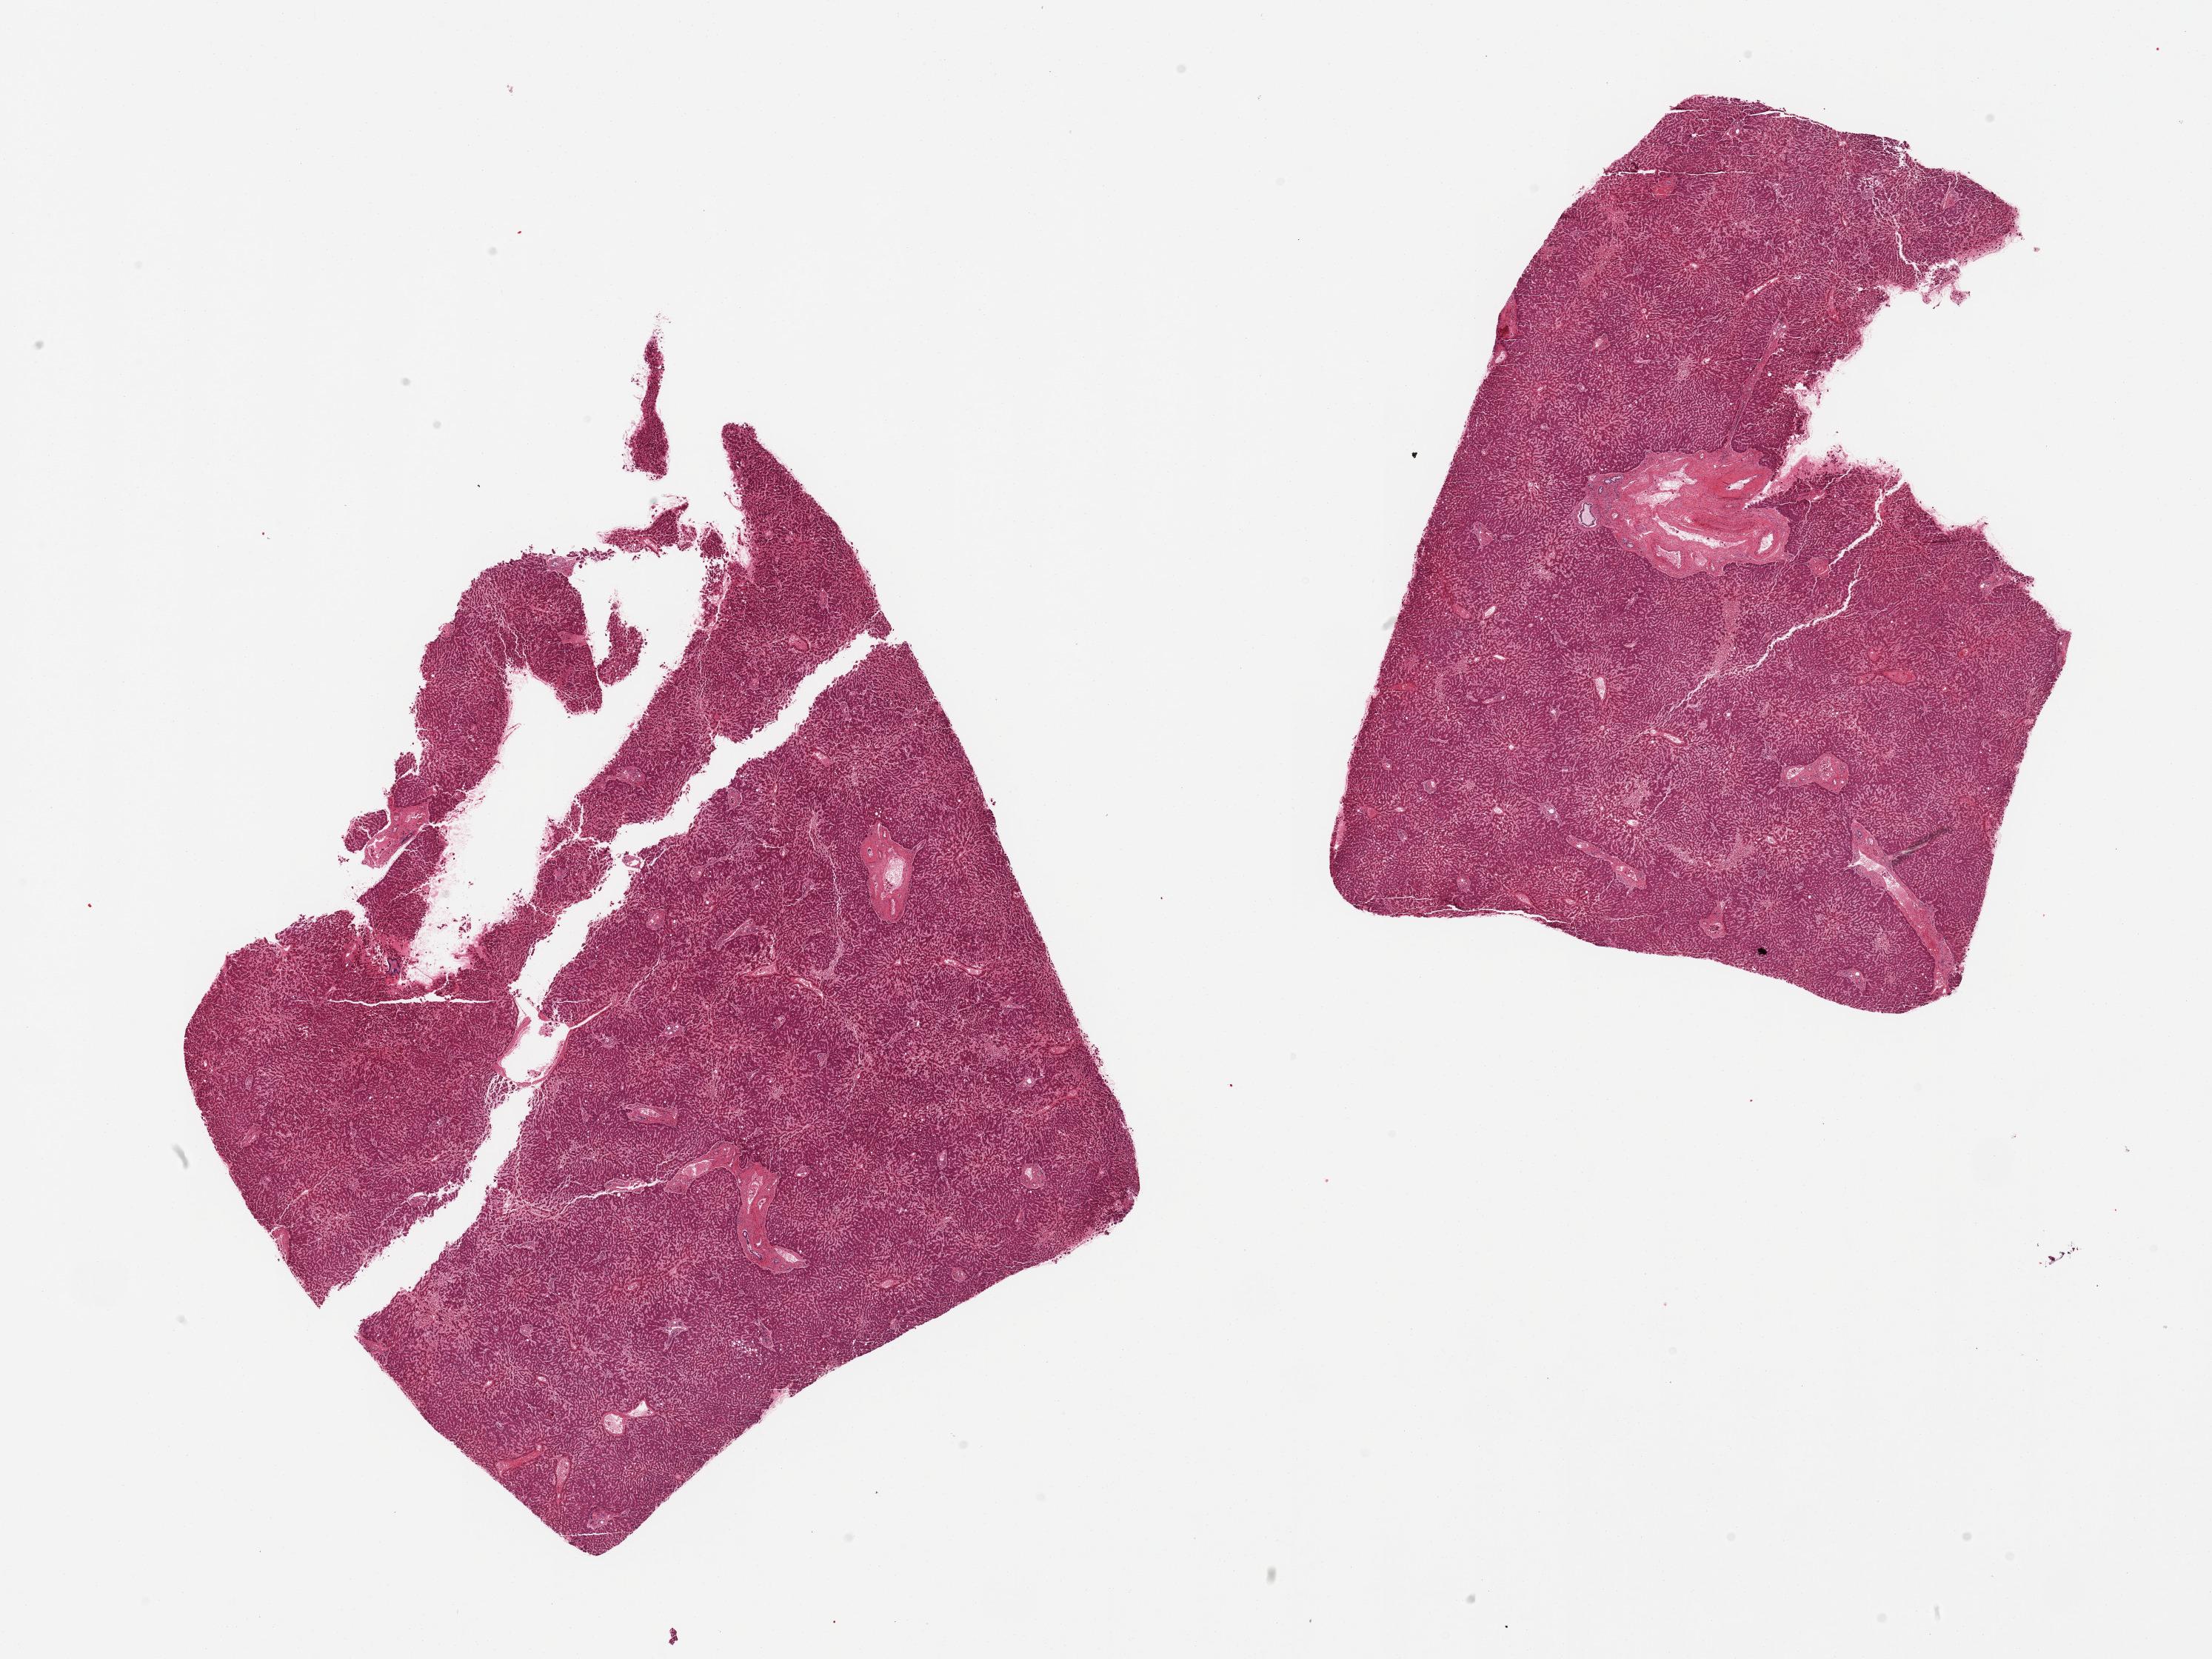
Digitized hematoxylin and eosin (H&E)-stained section — a low-resolution overview of the entire scanned area, about 23.6 x 17.7 mm (from a 20x scan). PAXgene-fixed, paraffin-embedded tissue. Section of liver (target tissue). Donor tissue sample. Donor sex: male.
• reviewer comment on this tissue sample: 2 pieces, moderate congestion, no steatosis/hepatitis noted